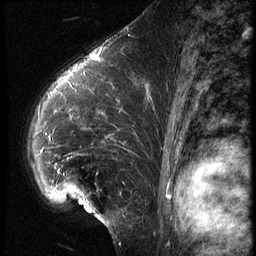
Breast MRI (dynamic contrast-enhanced), one sagittal slice; slice 41 of 62 in the series (ordered by position); 3 images stored at this slice position (order not interpretable as contrast timing); 1.5 T; TE 4.2 ms, TR 9 ms; 256 × 256 image matrix, field of view 180 × 180 mm. Female patient, age 39 years. From the clinical record (not read from this slice): setting: breast cancer imaged before/during neoadjuvant chemotherapy; receptor status: HER2-positive.
Structures marked on this image (semi-automatically segmented with operator editing):
- analysis volume of interest (the breast-tissue region the enhancement analysis was run in; not a lesion): bounding box <23,64,155,228> (left, top, right, bottom; pixels)
- tumour enhancement mask (voxels above the 140 % enhancement threshold inside the analysis volume of interest): <42,82,114,174>